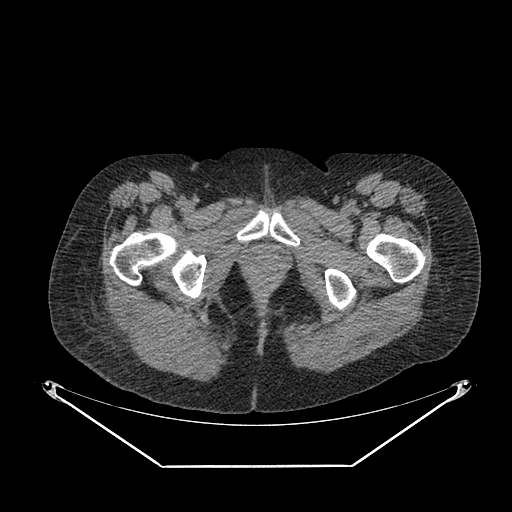
CT of an extremity soft-tissue mass (from a PET/CT study), one axial slice. Position 45 of 267 along the scan axis. Reconstruction kernel SOFT. 140 kVp. Soft-tissue window (W 400 / L 40 HU). 3.75 mm slice thickness. 512 × 512 image matrix, field of view 500 × 500 mm. Female patient. From the clinical record (not read from this slice): histological type: spindle cell suggestive of myxofibrosarcoma; grade: intermediate; site of the primary tumour: right buttock.
Structures marked on this image (expert contour drawn on MRI and transferred to this co-registered scan by the dataset authors):
- gross tumour volume (mass): bounding box <112,299,166,346> (left, top, right, bottom; pixels)